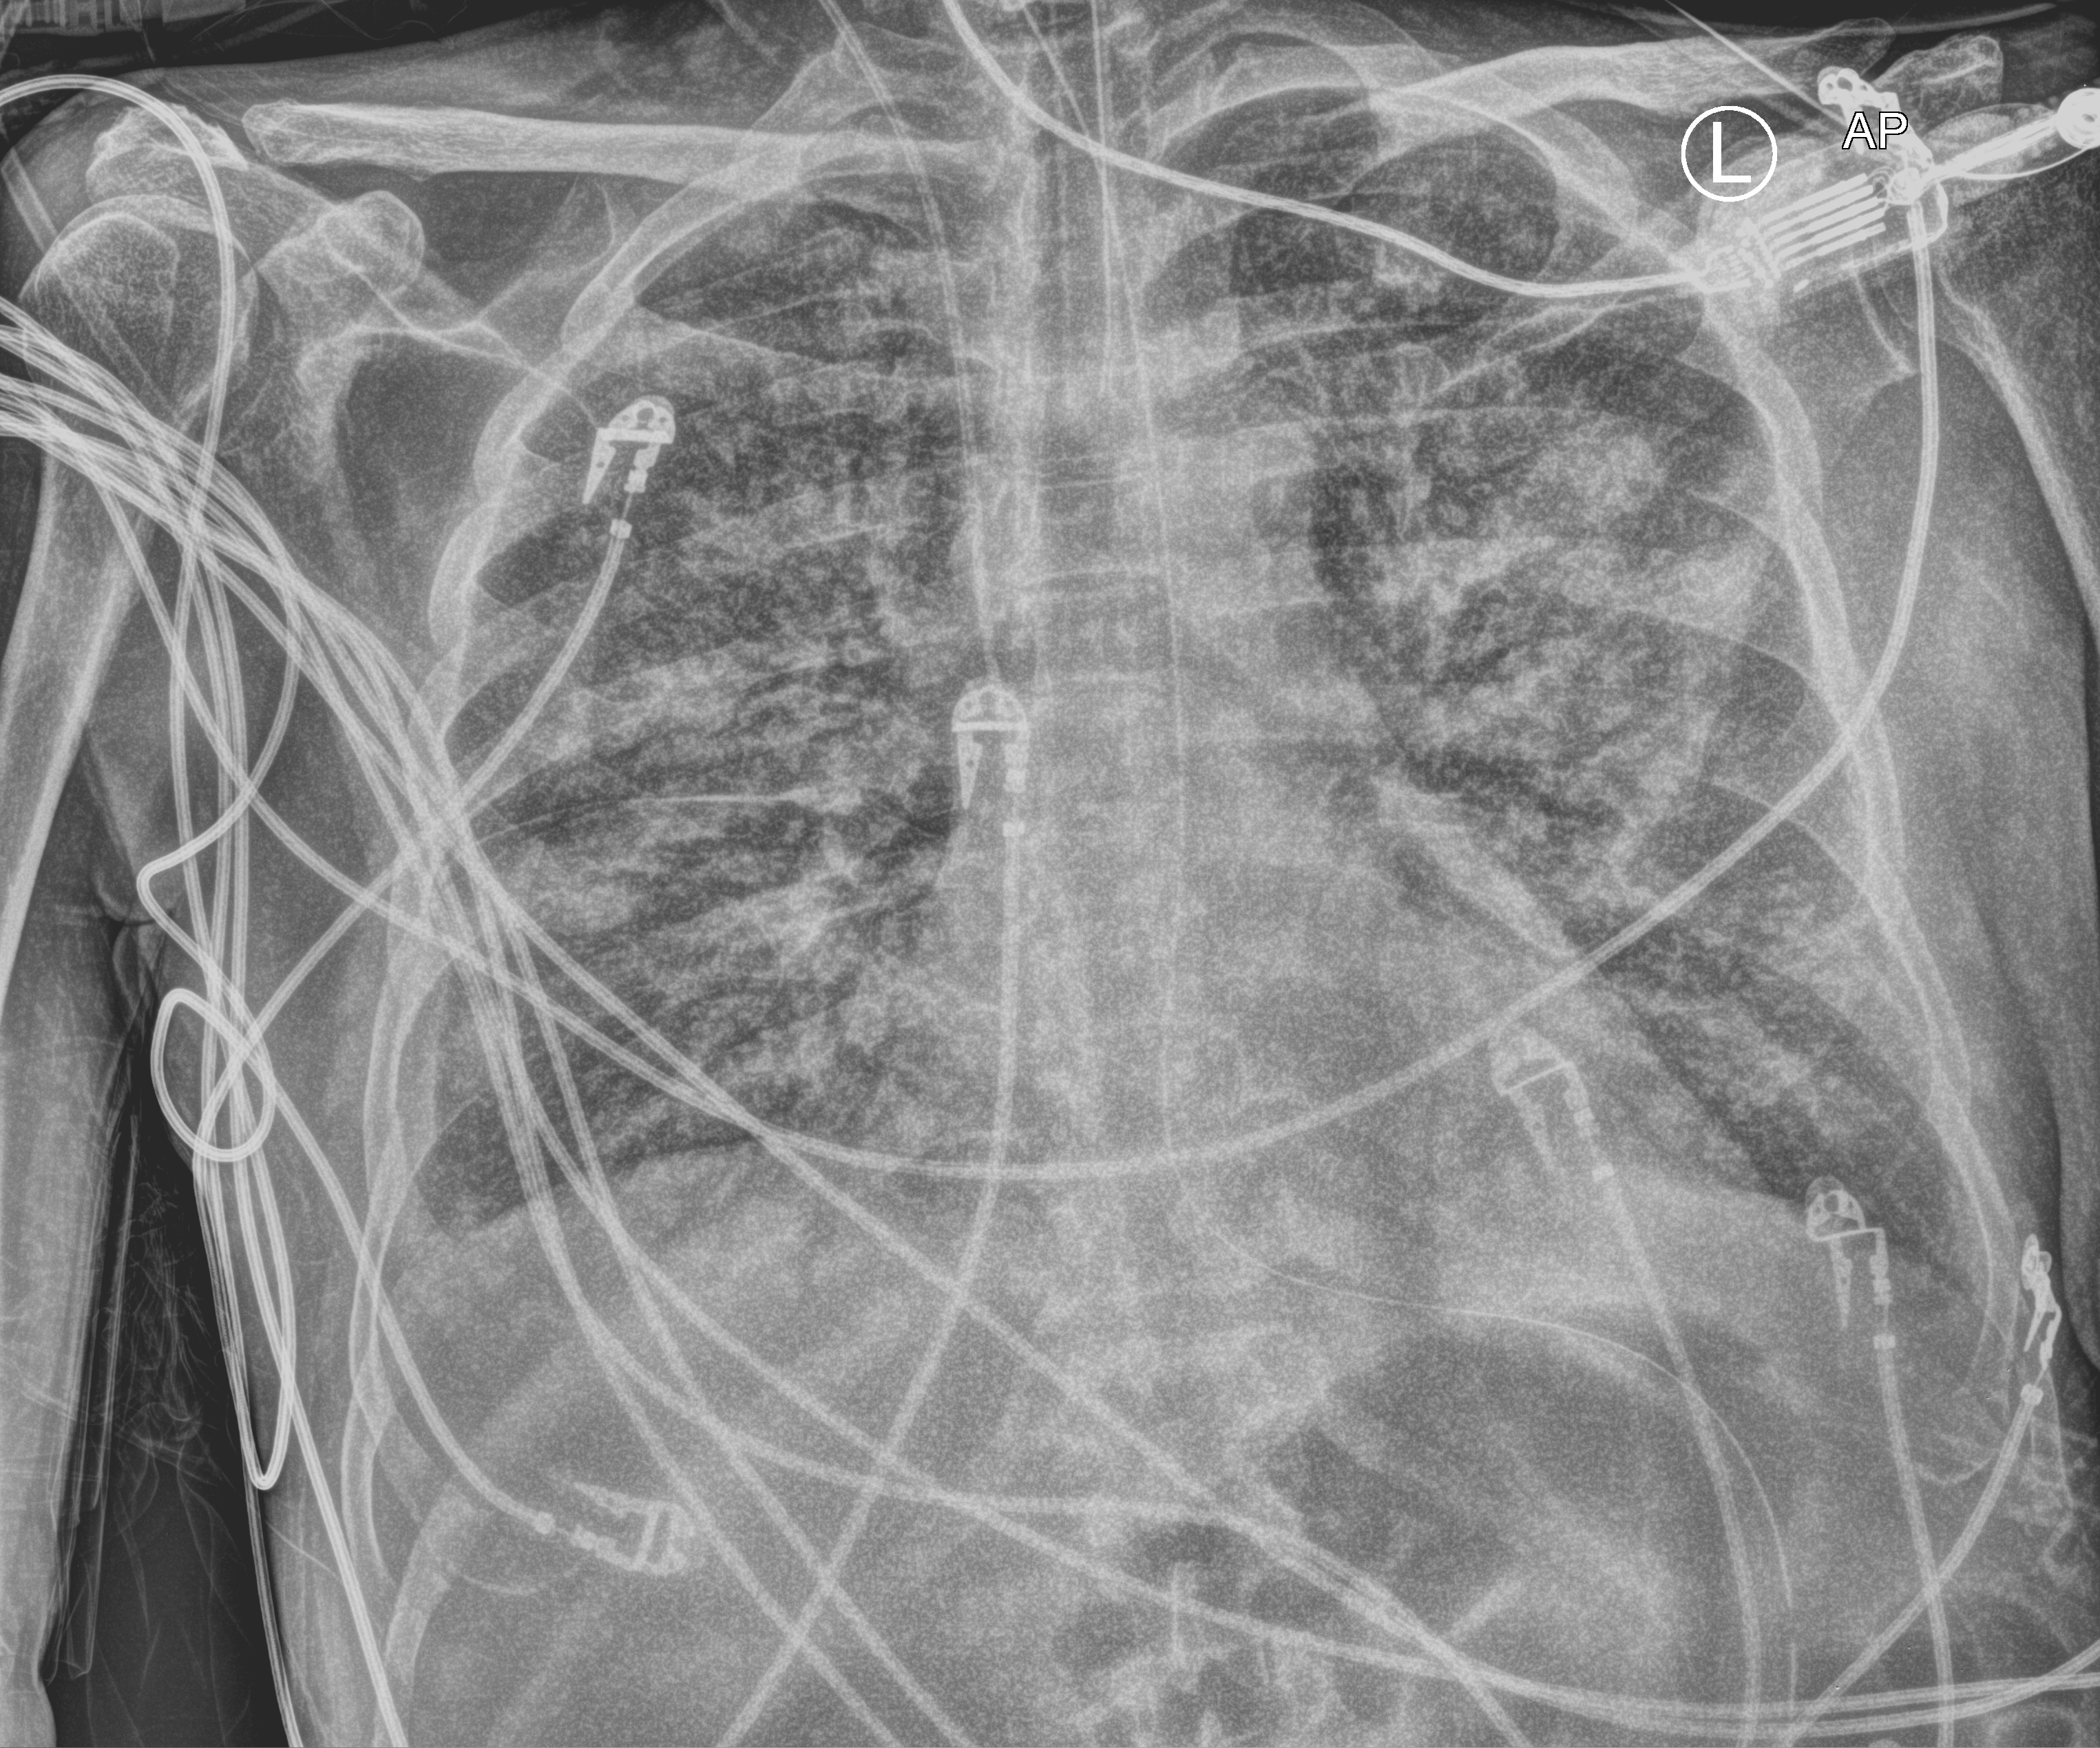
Chest X-ray (portable), anteroposterior (AP) projection. Male patient hospitalised with COVID-19, age 60–74 years.
From the hospital-stay record, not from the radiograph (when in the stay this image was taken is not recorded): length of hospital stay: 24 days.